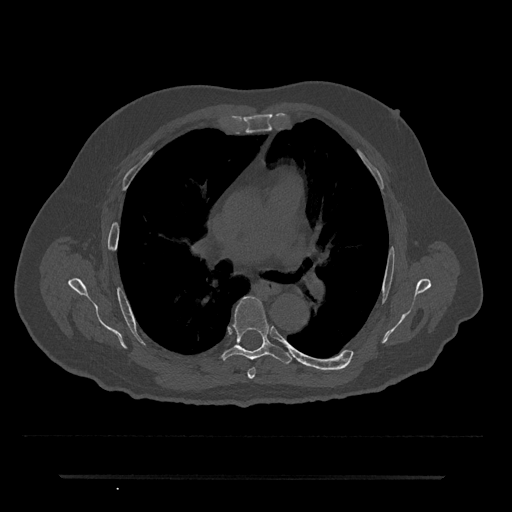
CT including the spine, one axial slice; position 442 of 797 along the scan axis; reconstruction kernel Br40s/3; bone window (W 1800 / L 400 HU); 0.5 mm slice thickness; 512 × 512 image matrix, field of view 437 × 437 mm. Patient: male, 69 years. Case-level facts recorded for this patient, not image findings: primary cancer: prostate.
Annotated regions visible in this slice (semi-automatically segmented with operator editing):
- T5 vertebra: box from (x=248, y=368) to (x=256, y=379) px
- T6 vertebra: (x=220, y=297)–(x=292, y=364)